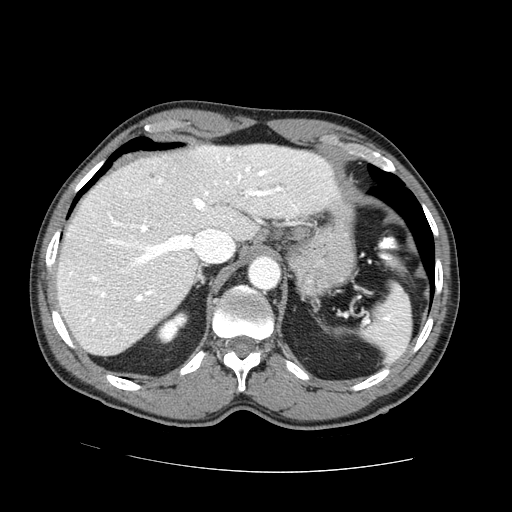
Contrast-enhanced abdominal CT (liver protocol), one axial slice; slice 53 of 73 in the series (ordered by position); 100 kVp; one of 2 acquisitions stored at this slice position; soft-tissue window (W 400 / L 40 HU); 2.5 mm slice thickness; 512 × 512 image matrix. Case-level facts recorded for this patient, not image findings: diagnosis: hepatocellular carcinoma (patient treated with transarterial chemoembolisation; whether this scan precedes or follows treatment is not stated here); TNM stage (as recorded): Stage-IVA; Child-Pugh class: A; tumour differentiation: no biopsy.
Structures marked on this image (semi-automatically segmented with operator editing):
- liver parenchyma outside the tumour (the mass and vessels are separate outlines, so this box may not span the whole liver): box from (x=56, y=144) to (x=340, y=356) px
- mass: (x=148, y=172)–(x=155, y=178)
- liver vessels: (x=69, y=155)–(x=297, y=321)